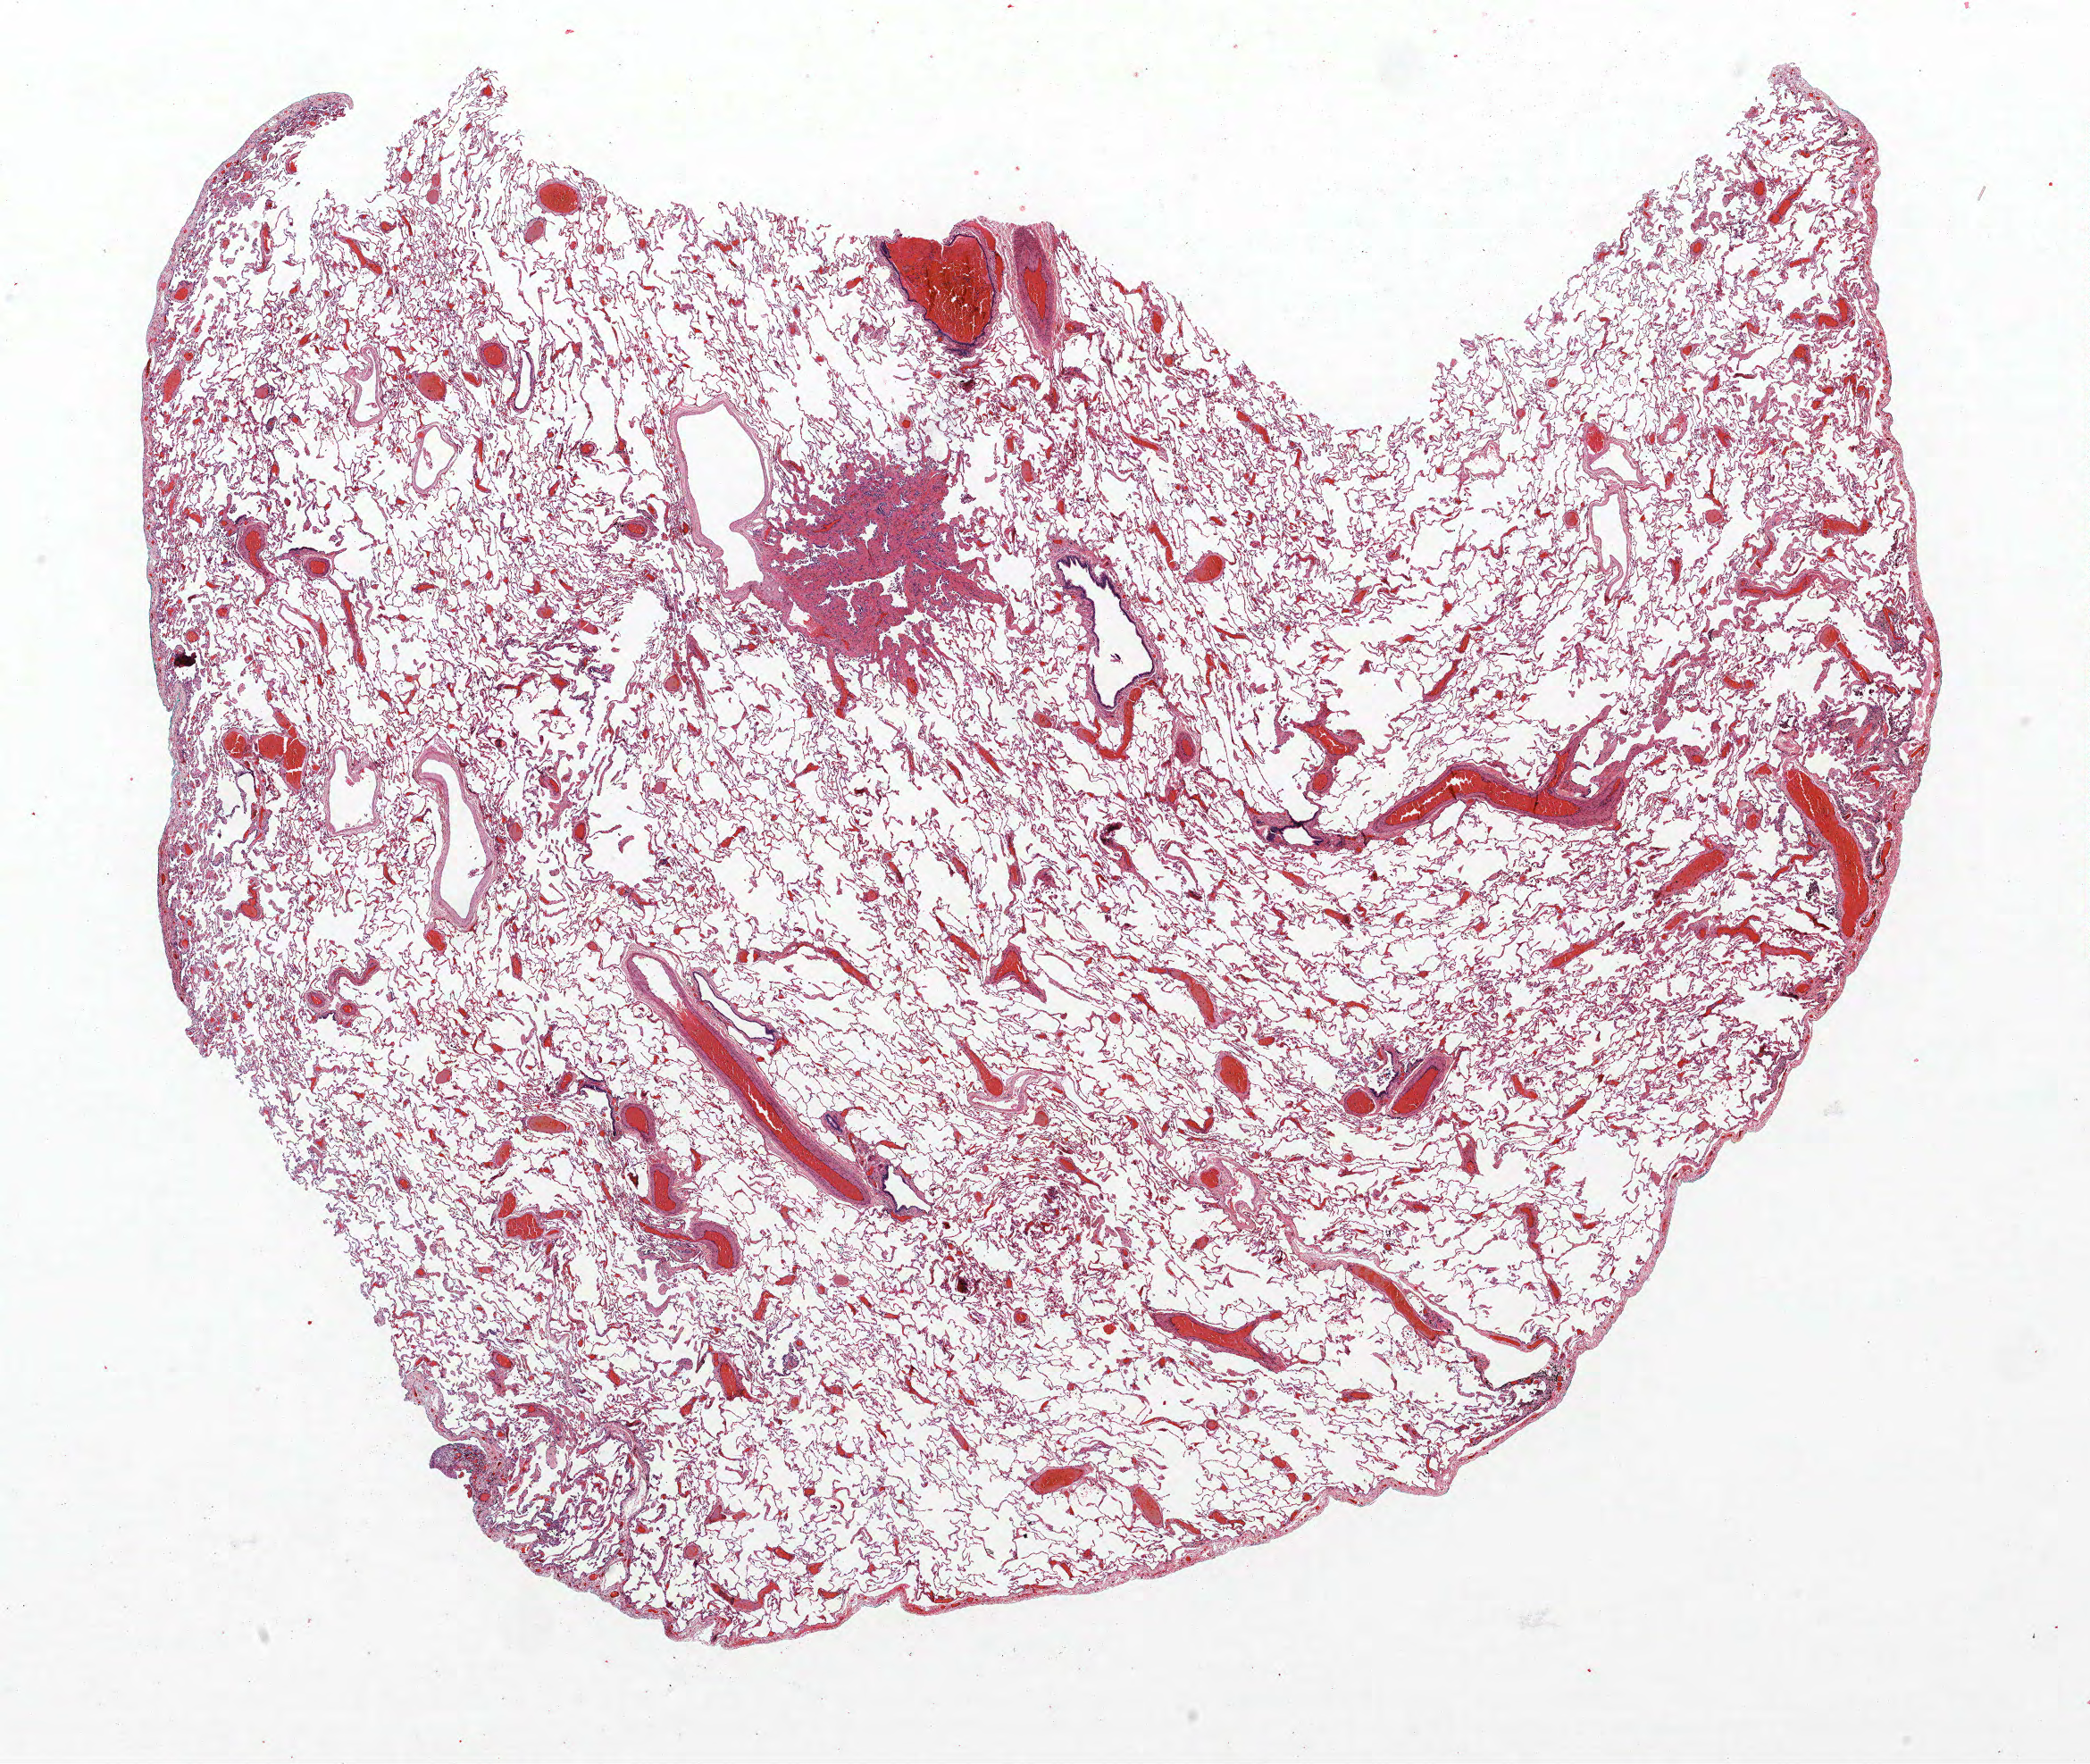
H&E-stained whole-slide image, shown as a low-resolution overview of the whole scanned area (about 18.7 x 15.8 mm). FFPE section. Lung tissue. Female, age 56 at enrolment. Grade: poorly differentiated (G3).
- tumour size (pathology): 20 mm
- participant's lung-cancer diagnosis: Adenocarcinoma, NOS
- primary tumour location (clinical record): right upper lobe
- ICD-O-3 topography: upper lobe of lung (C34.1)
- stage (AJCC 6th edition): IA